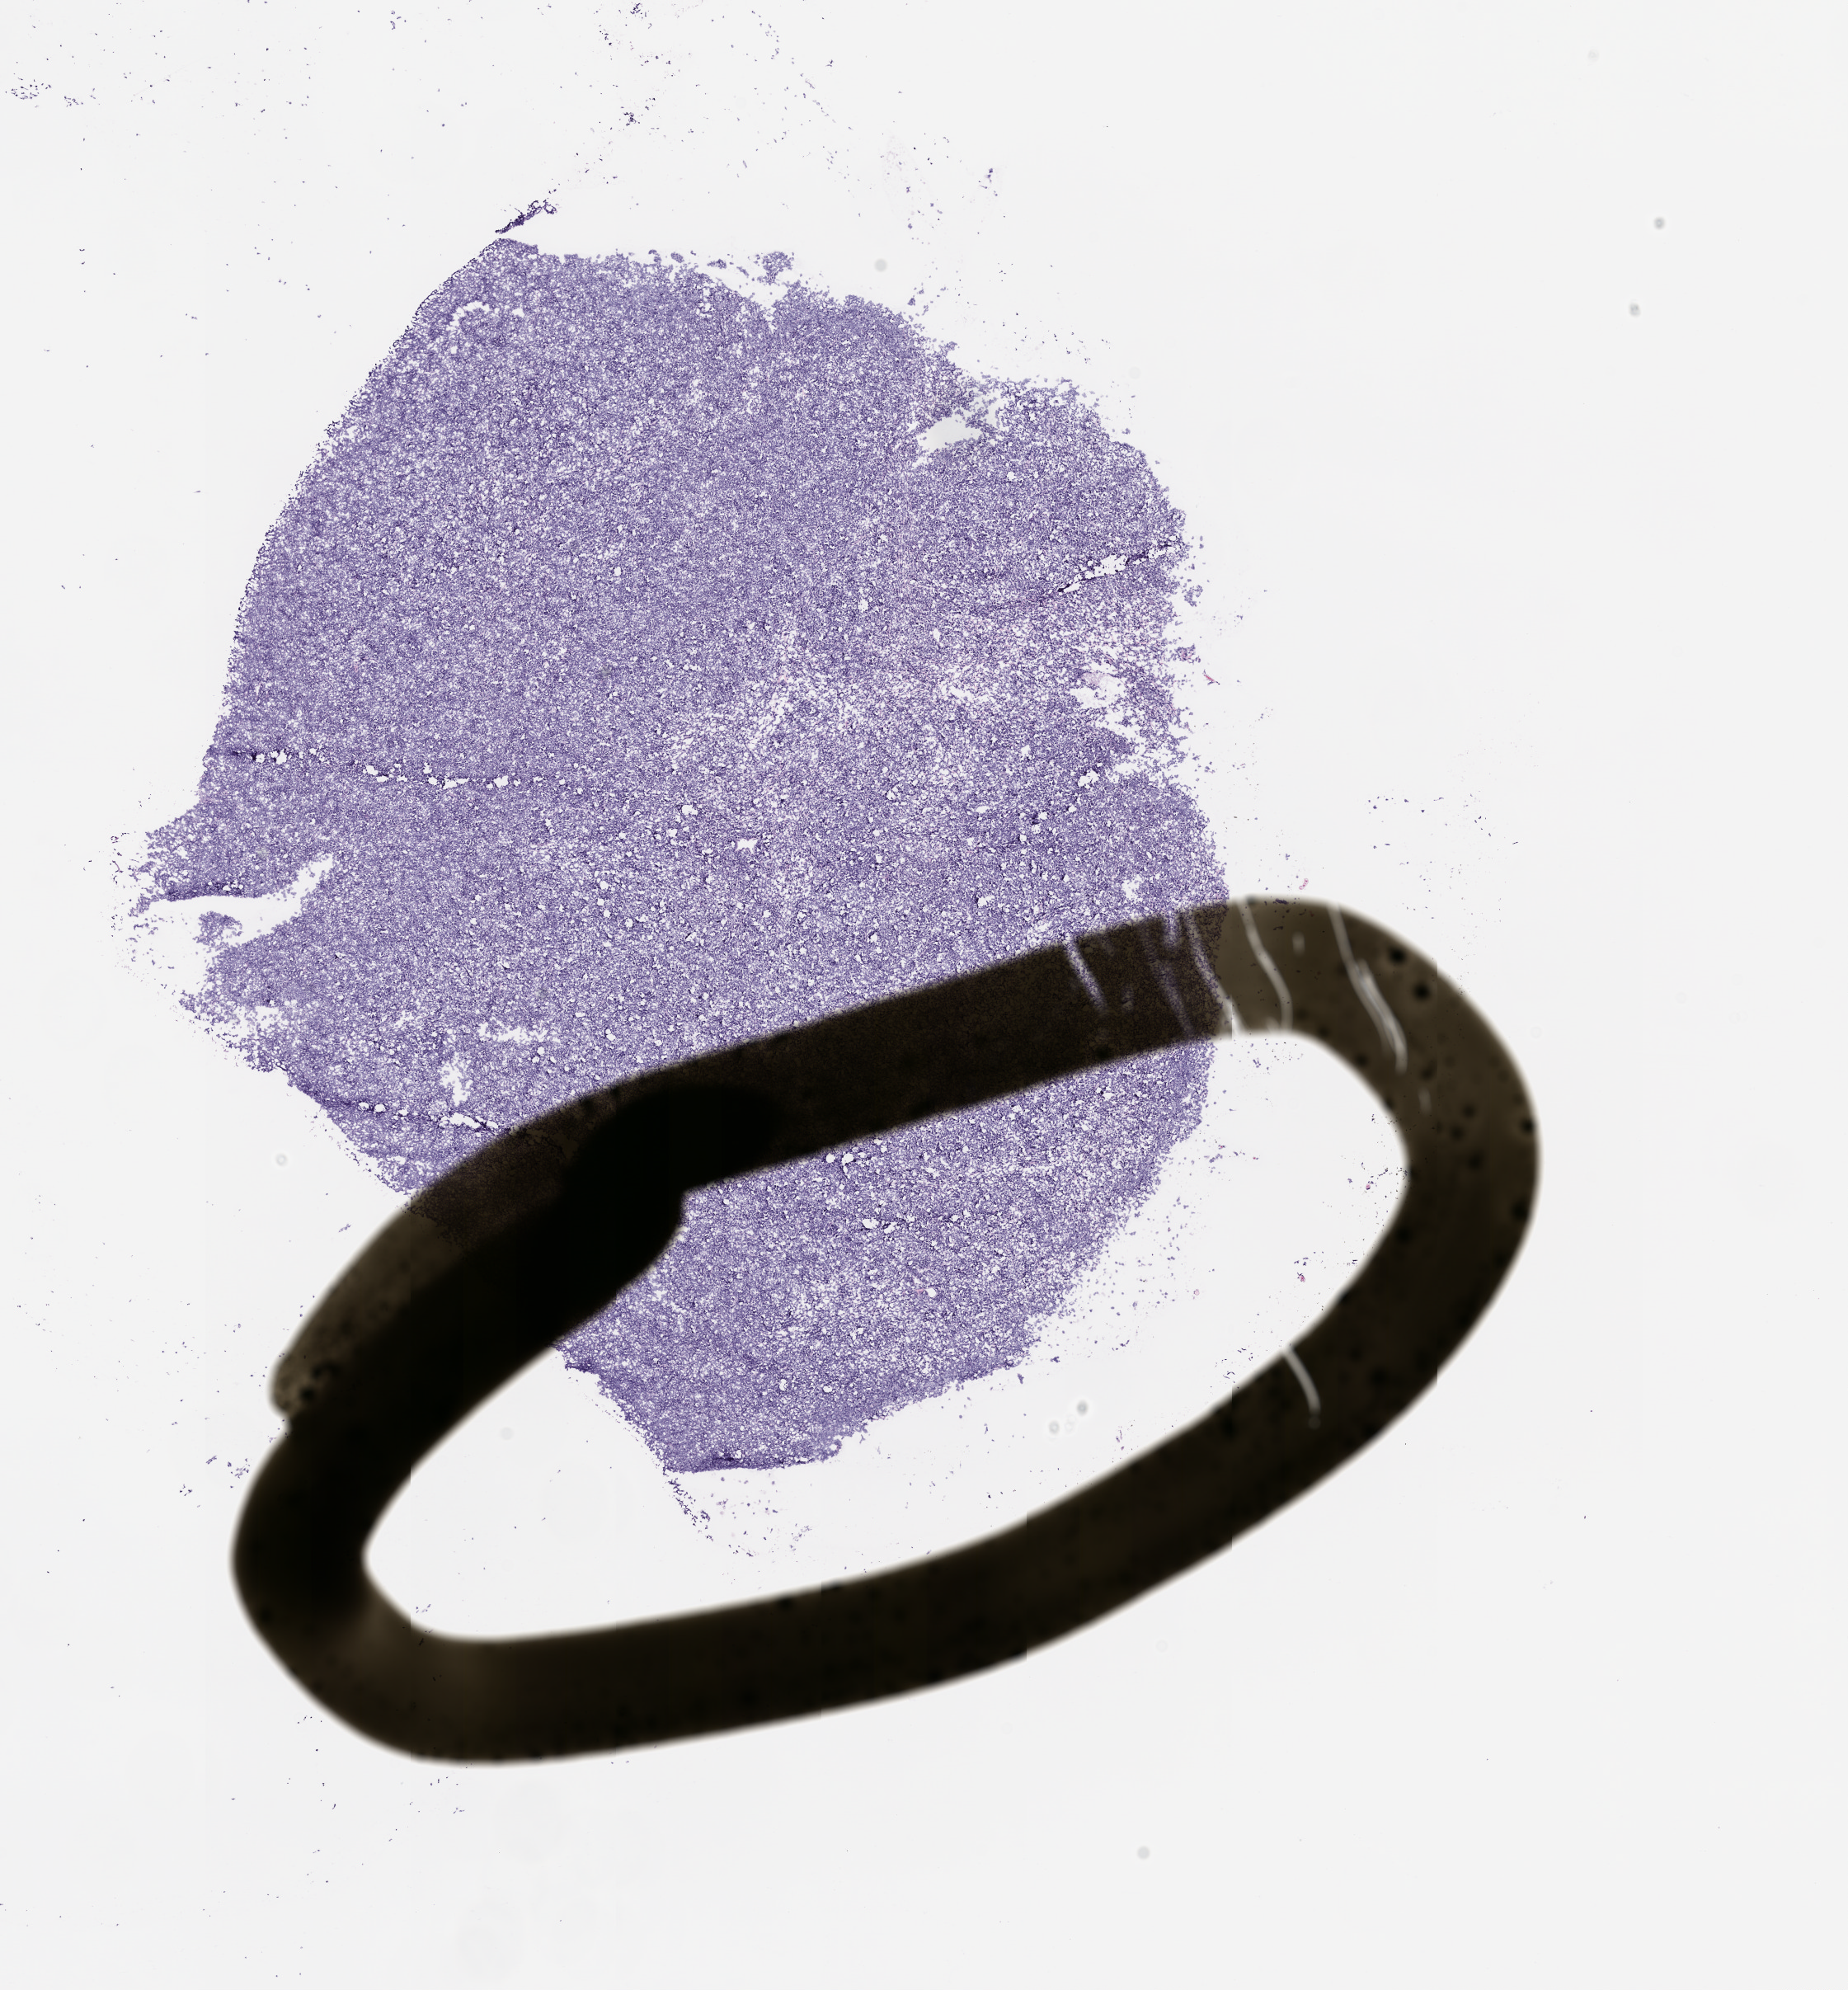
H&E whole-slide image of a patient-derived xenograft (PDX) tumor grown in a mouse, passage 1 — shown as a low-resolution overview of the whole scanned area (about 9.0 x 9.7 mm); FFPE section; tumor site category: musculoskeletal.
Originating patient diagnosis: Synovial Sarcoma.